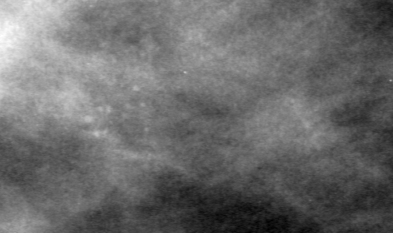
Cropped region of a digitized screen-film mammogram centred on a radiologist-marked abnormality; left breast; CC view.
- Calcifications, morphology pleomorphic, distribution clustered; BI-RADS assessment category 4; pathology (as recorded): benign.